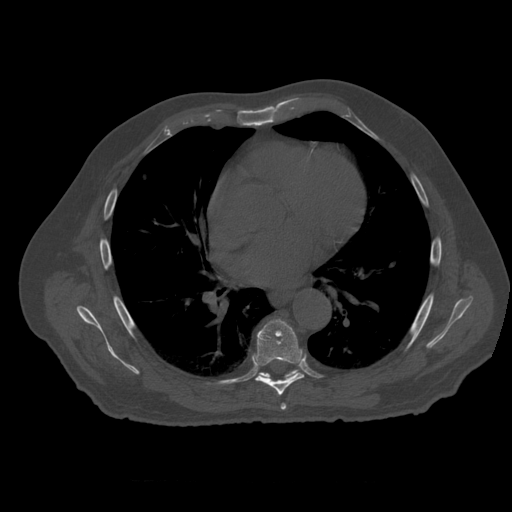
CT including the spine, one axial slice. Position 357 of 399 along the scan axis. 120 kVp. Bone window (W 1800 / L 400 HU). 512 × 512 image matrix, field of view 407 × 407 mm. Patient age 73 years. From the clinical record (not read from this slice): primary cancer: prostate; vertebrae with lytic lesions (as recorded): L2.
Annotated regions visible in this slice (semi-automatic segmentation, software-assisted and operator-edited):
- T6 vertebra: bounding box (x1, y1, x2, y2) in pixels: (281, 404, 287, 410)
- T7 vertebra: (253, 319, 304, 396)
- T8 vertebra: (261, 370, 299, 379)